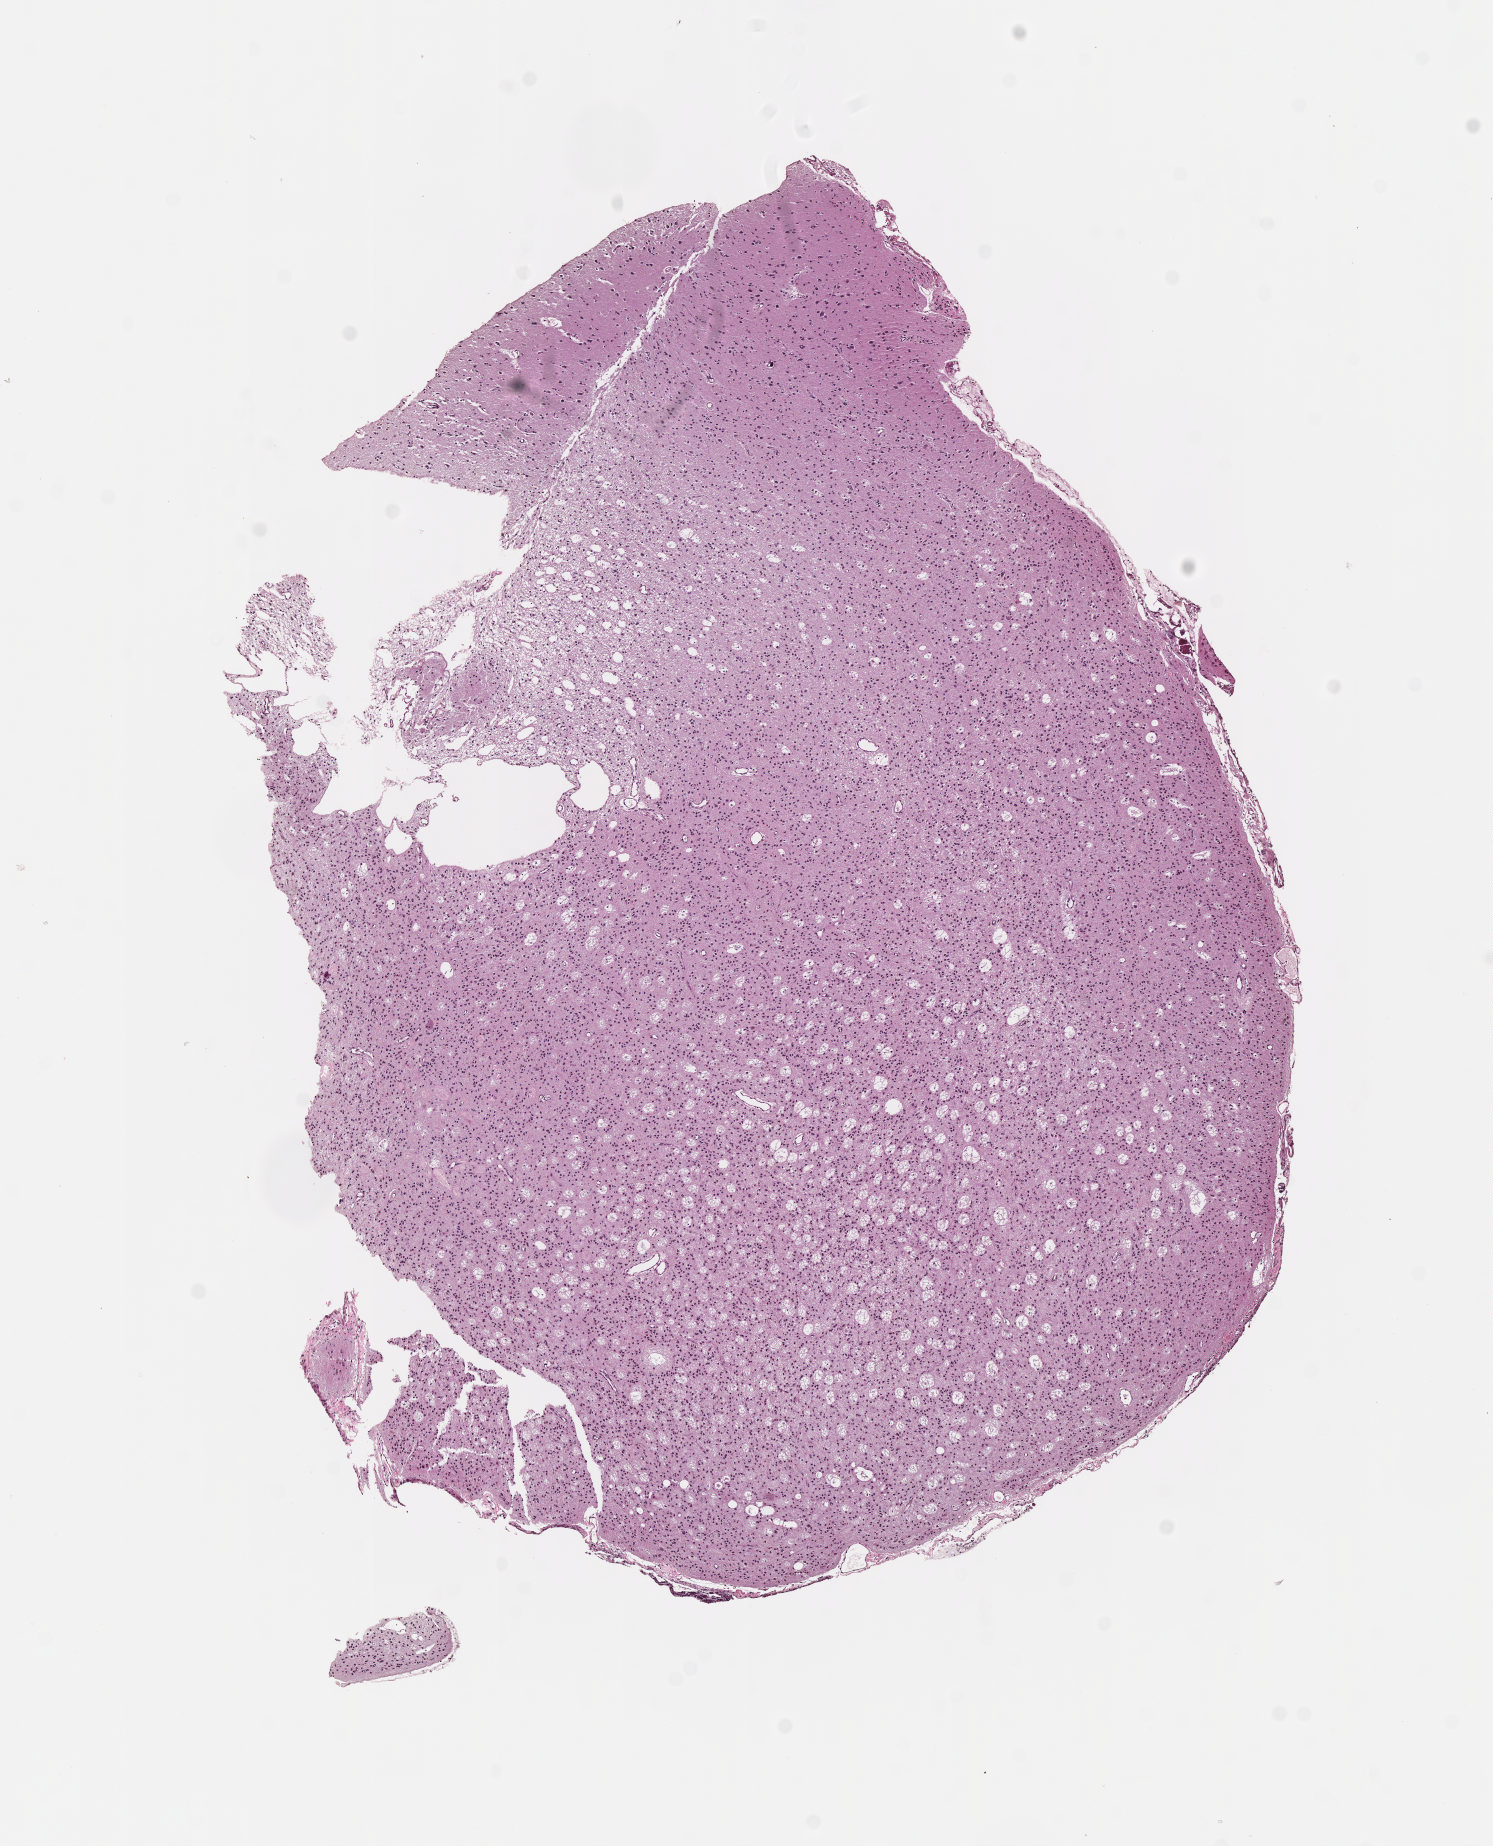
Digitized H&E-stained tissue section (whole slide) — whole scanned area (about 6.0 x 7.5 mm, from a 40x scan) shown as a low-resolution overview; formalin-fixed paraffin-embedded (FFPE) diagnostic section; sample: primary tumour, brain. Patient: male, age at initial diagnosis 51 years. Histologic grade: G3 (poorly differentiated).
Pathologic diagnosis: Oligodendroglioma, anaplastic (cerebrum).